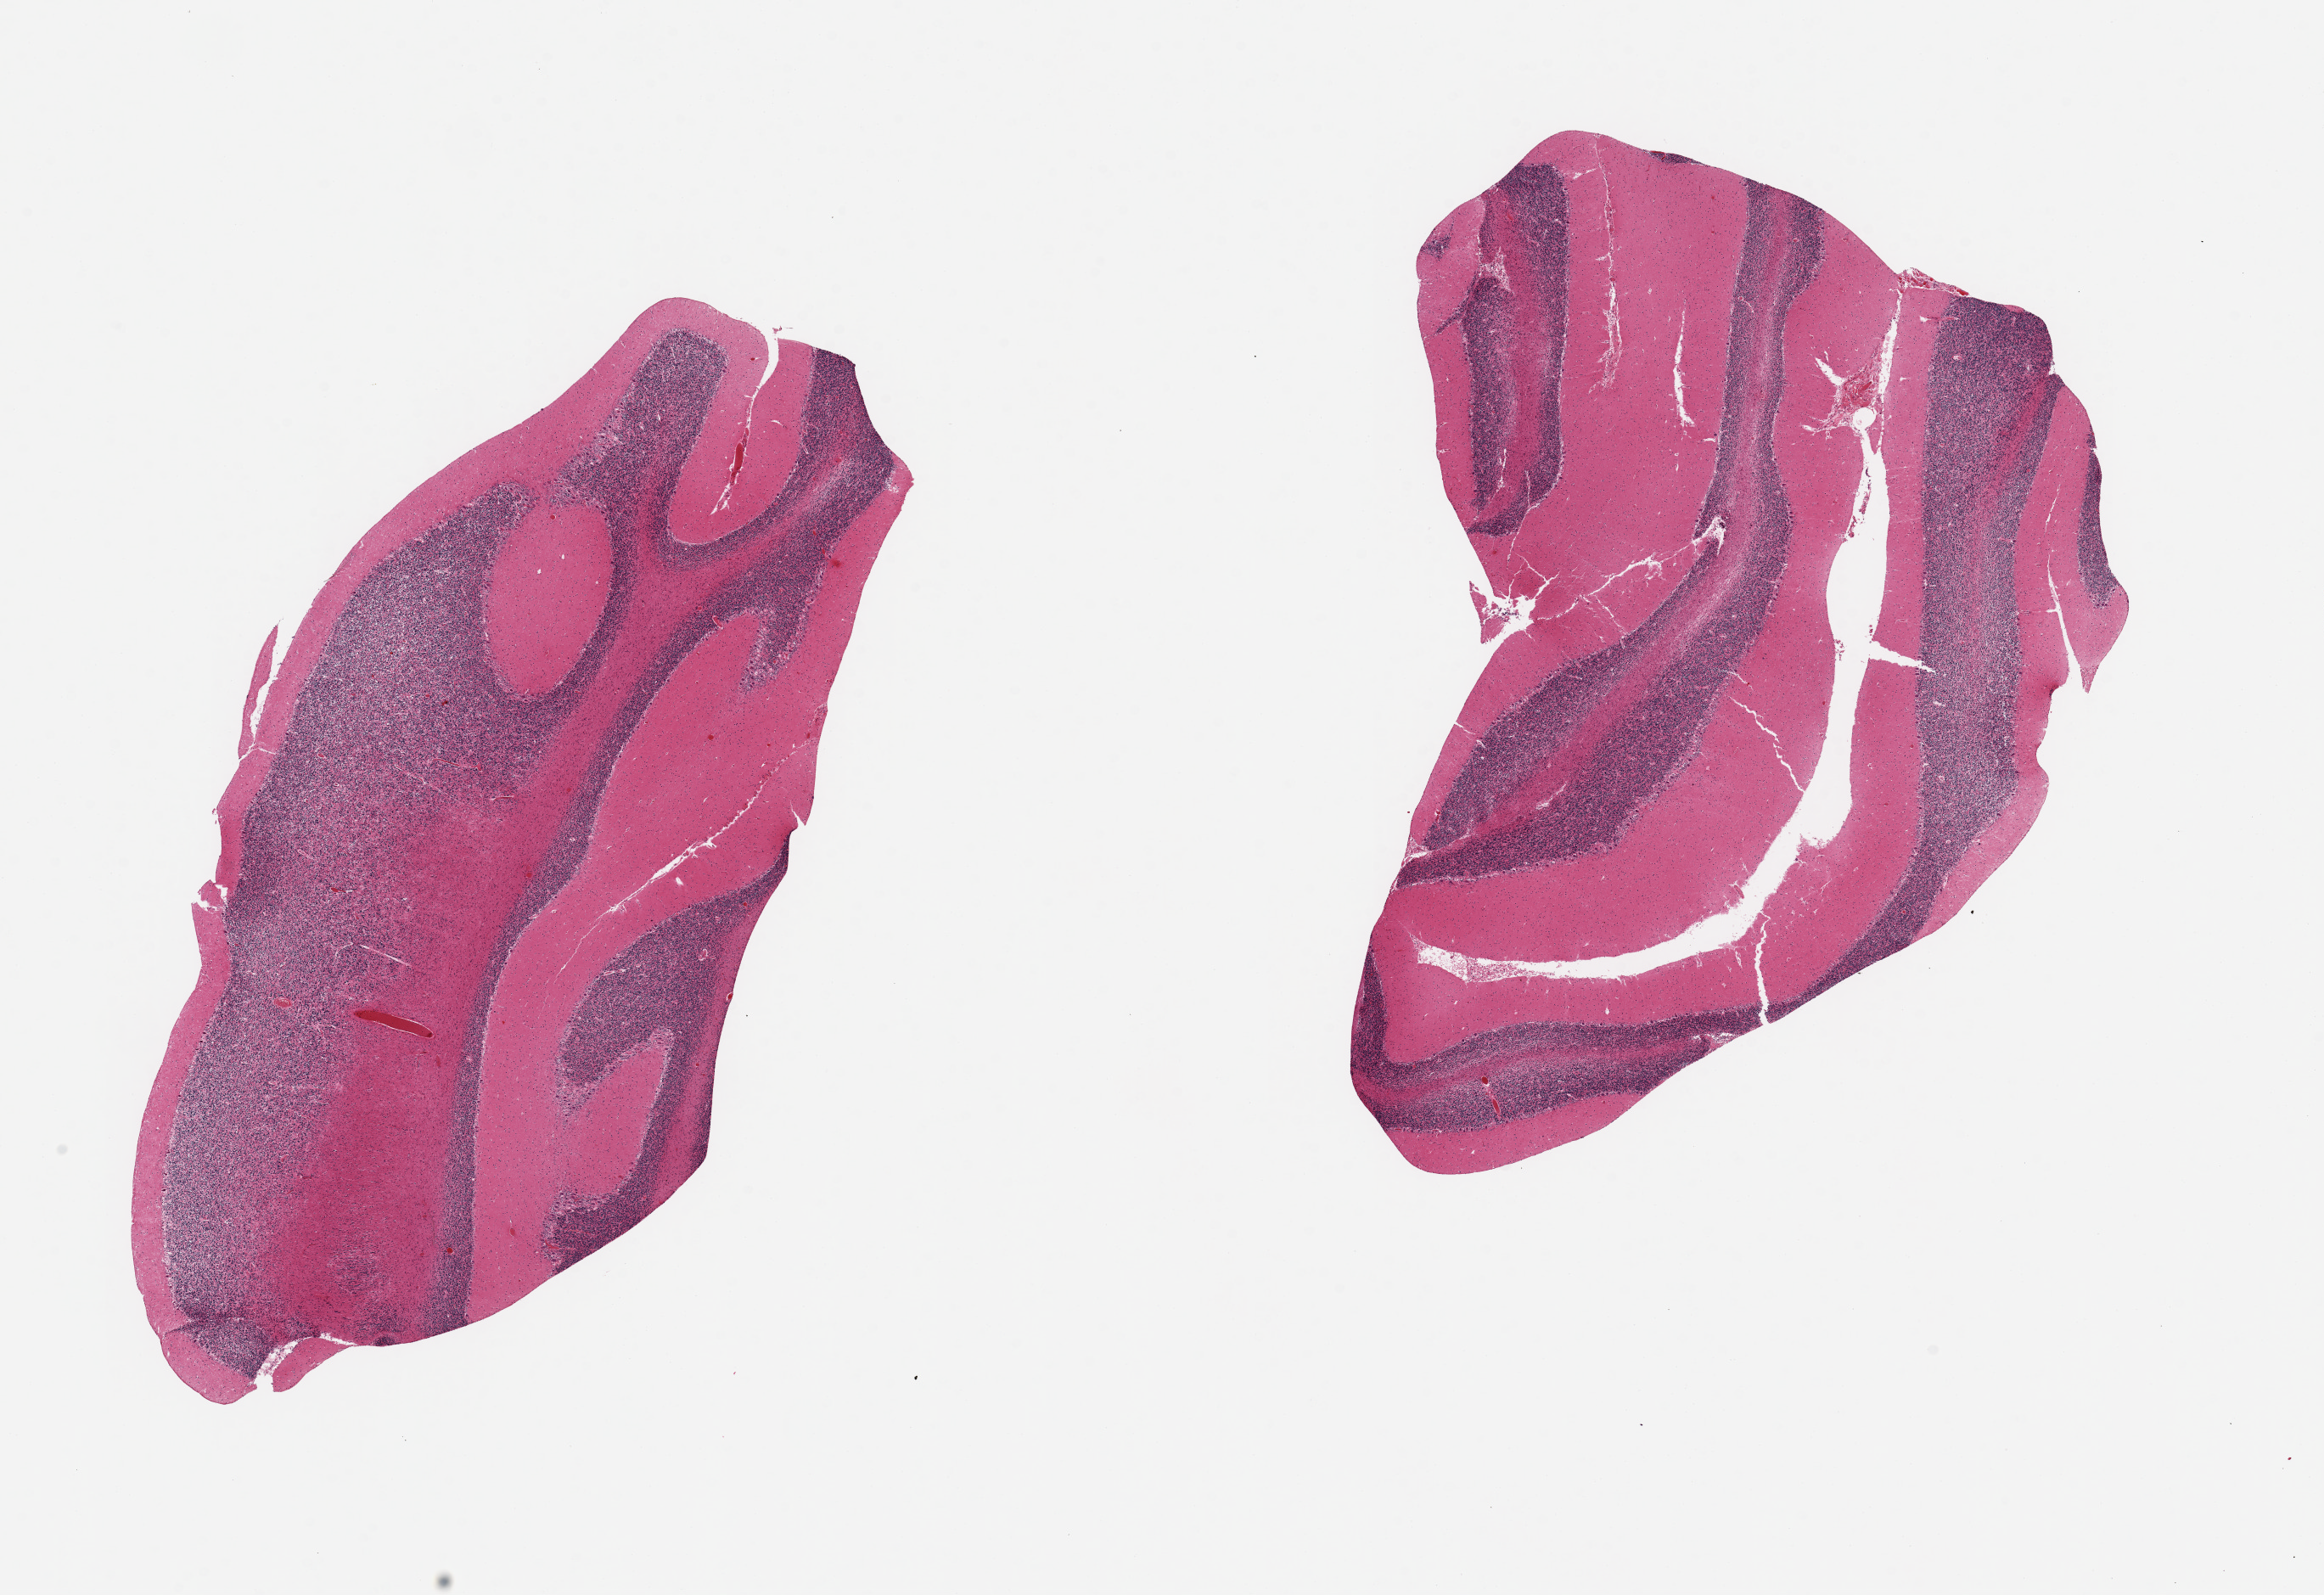
Digitized haematoxylin and eosin-stained section, brightfield — whole scanned area (about 21.7 x 14.9 mm, slide scanned at 20x) shown as a low-resolution overview, PAXgene-fixed, paraffin-embedded tissue, section of cerebellum (target tissue), tissue donor sample. Donor sex: male.
• review note (as recorded): 2 pieces, no abnormalities